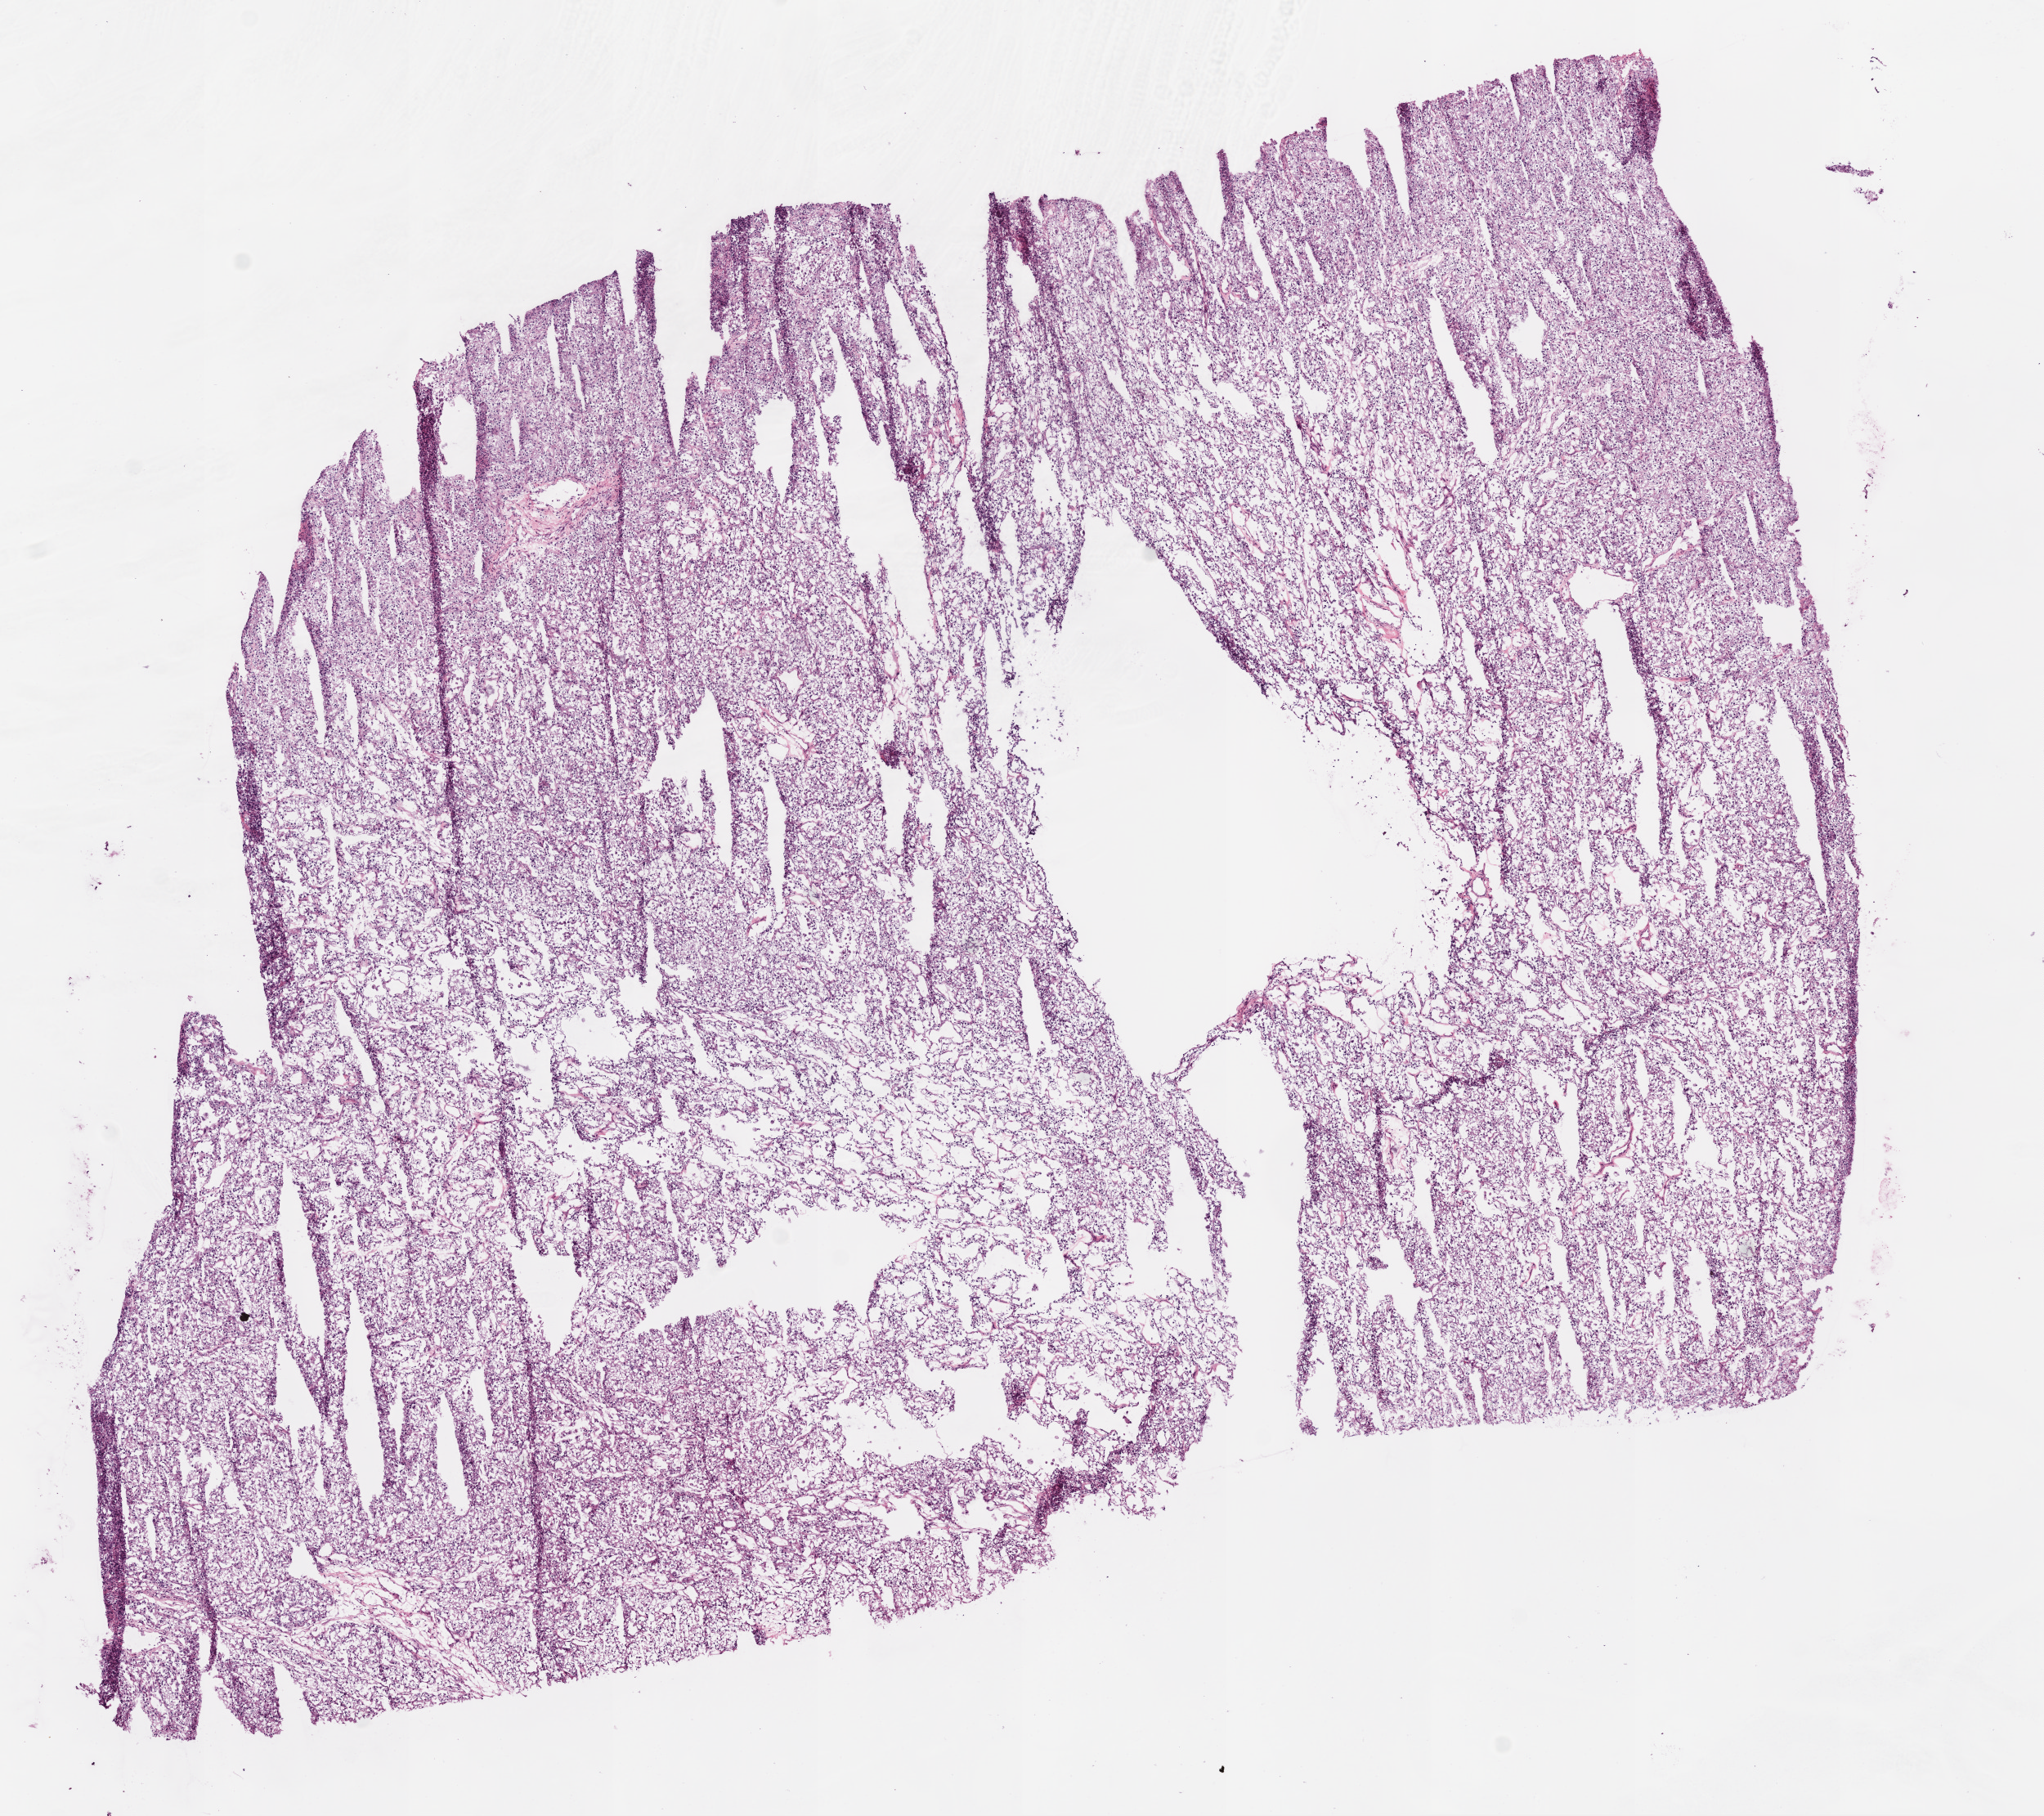
Digitized H&E tissue section (whole slide) — low-resolution overview of the scanned area, about 10.0 x 8.9 mm (from a 20x scan). Frozen section from the bottom of the tissue portion. Sample: primary tumour, kidney. Male patient; age at initial diagnosis 40 years. Histologic grade: G2 (moderately differentiated). Composition of this section per pathologist review: tumour cells 95%, tumour nuclei 80%, normal cells 0%, stromal cells 5%, necrosis 0%.
* pathologic diagnosis: Clear cell adenocarcinoma, NOS
* AJCC pathologic stage: IV (6th edition)
* TNM: T2 N0 M1
* laterality: left
* lymph nodes positive (case pathology): 0 of 22 examined